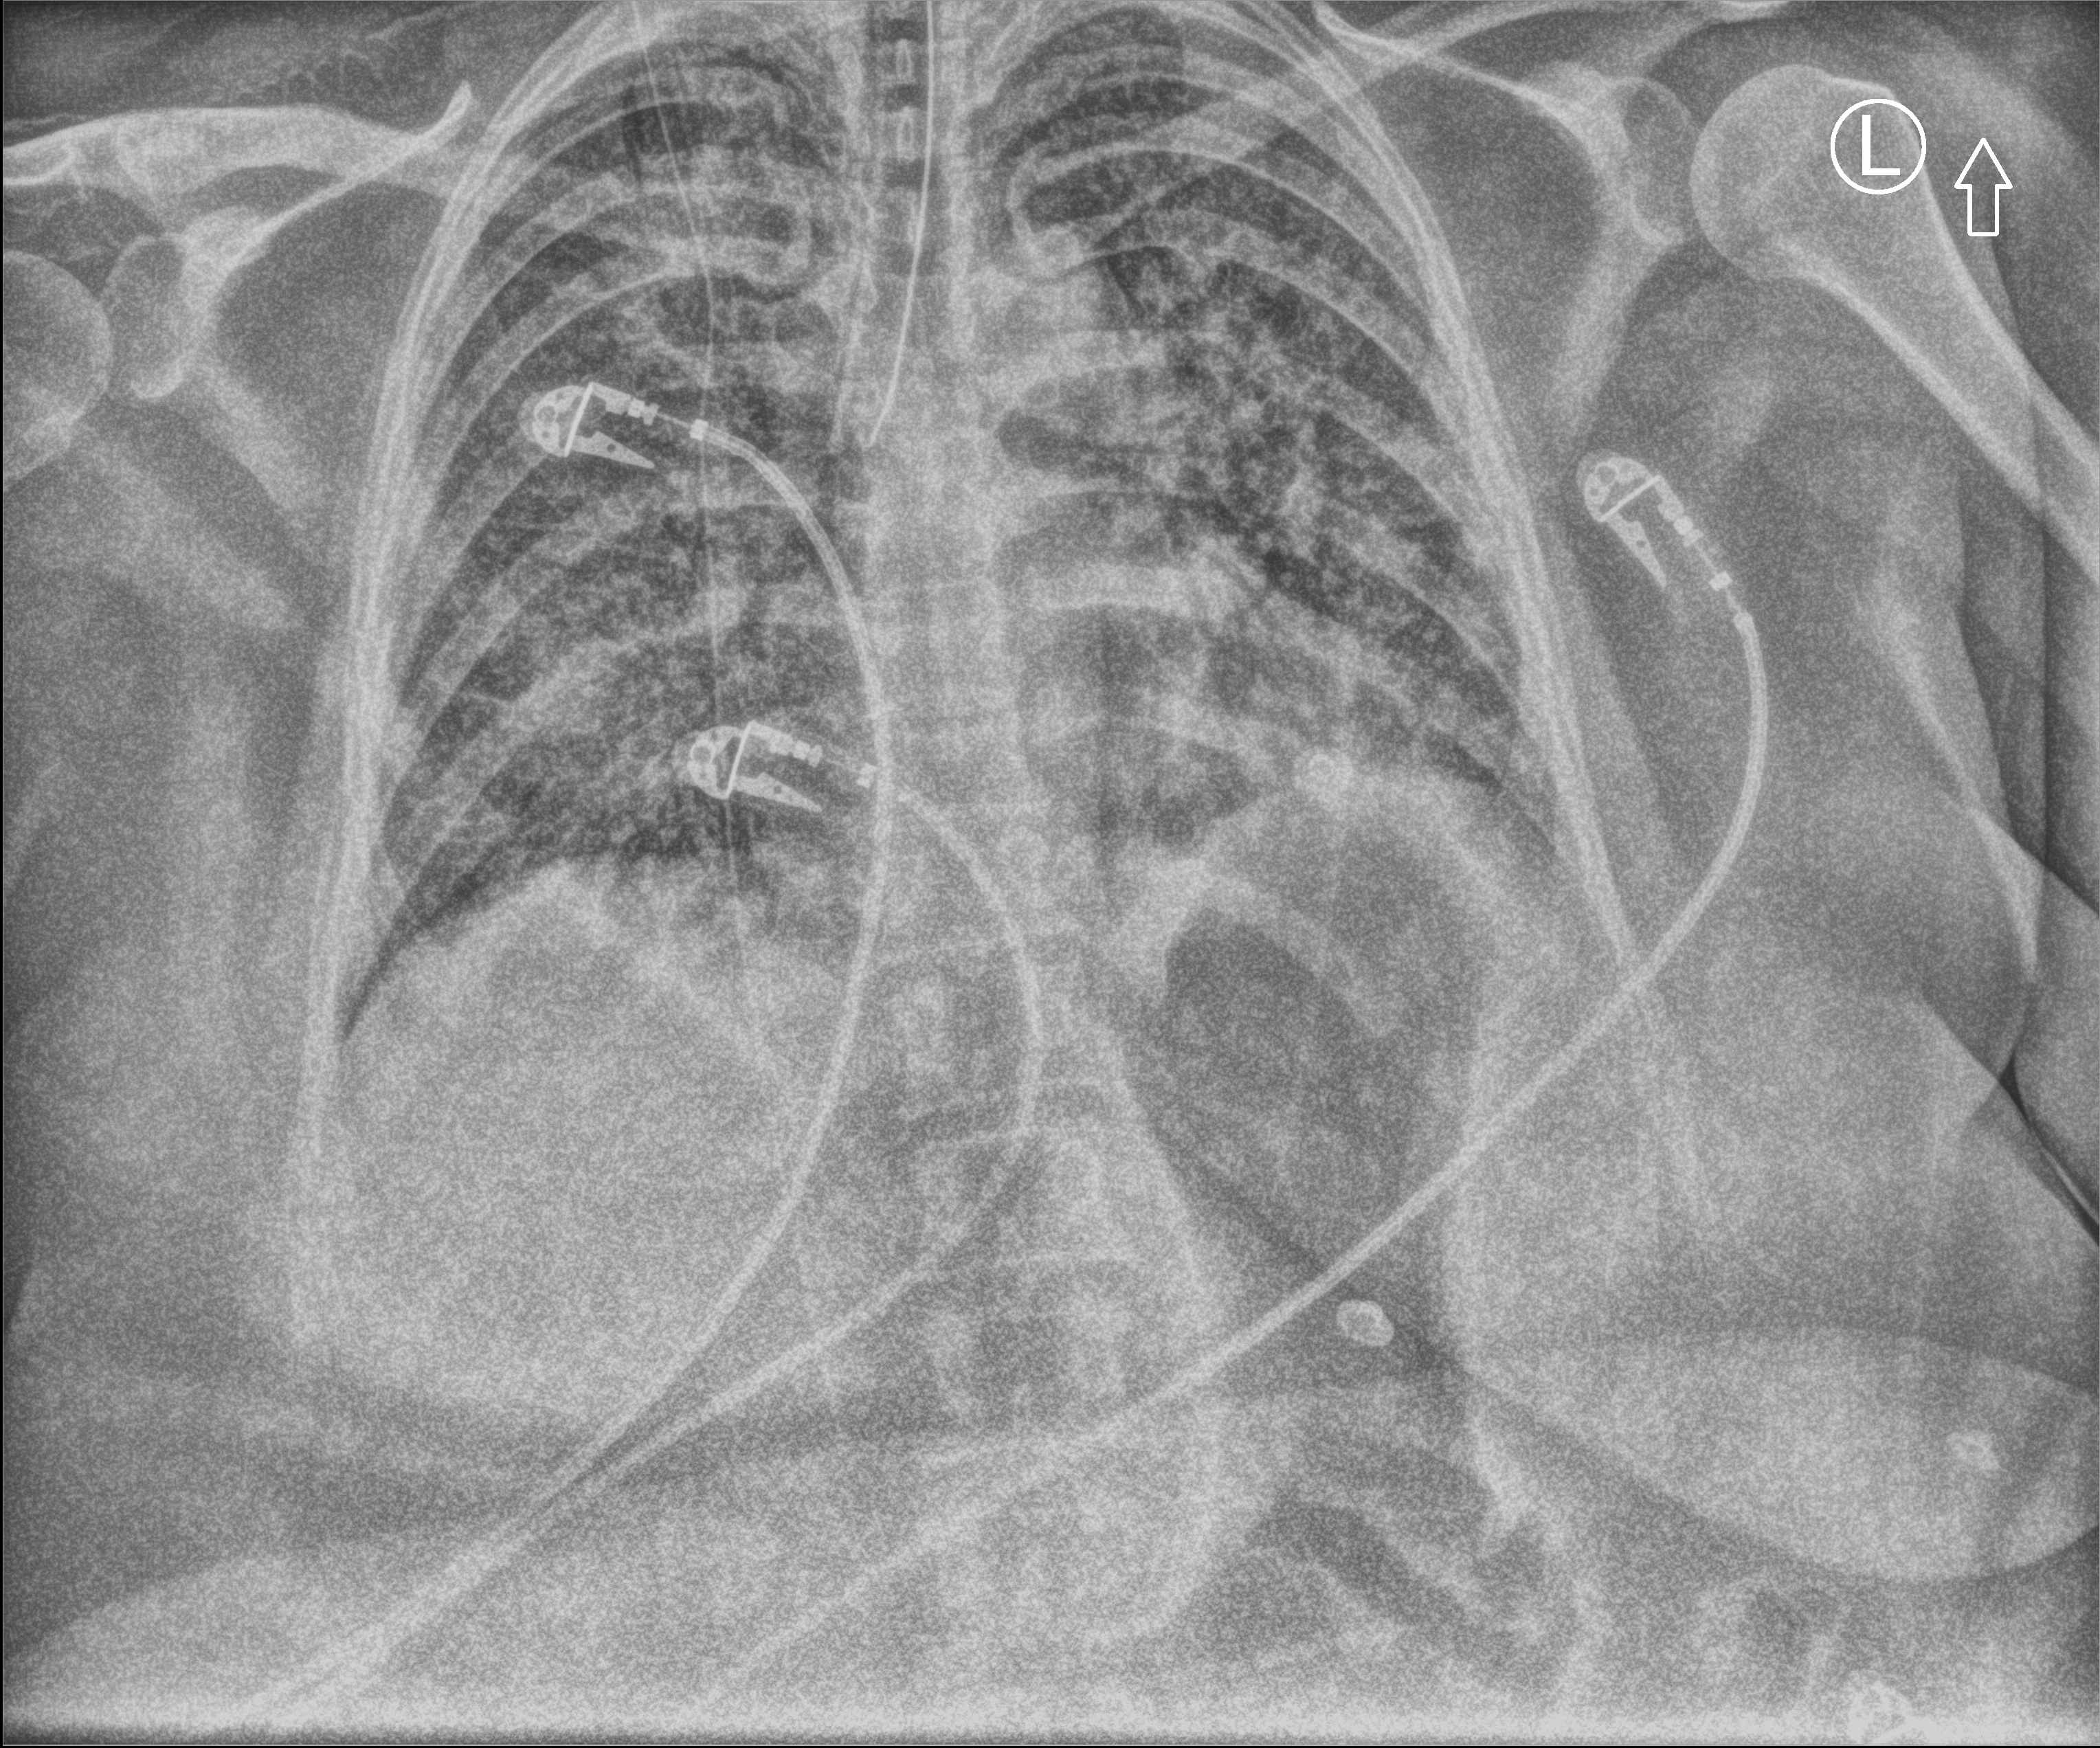
Bedside chest radiograph (computed radiography). Patient hospitalised with COVID-19; female, aged 18–59 years.
Hospital-stay facts (about this admission, not read from this image; timing relative to this image not recorded):
- admitted to intensive care during this hospital stay: yes
- mechanically ventilated during this hospital stay: yes
- length of hospital stay: 95 days